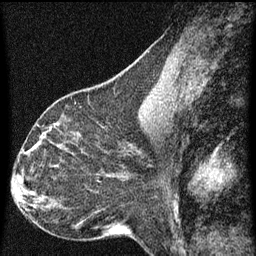
Breast MRI (dynamic contrast-enhanced), one sagittal slice. Slice 31 of 60 in the series (ordered by position). Dynamic contrast-enhanced series, image 2 of 3 at this slice position (ordered by acquisition). 1.5 T. TE 4.2 ms, TR 8 ms. 256 × 256 image matrix. Patient: female, 44 years.
Outlined on this slice (semi-automatically segmented with operator editing):
- analysis volume of interest (the breast-tissue region the enhancement analysis was run in; not a lesion): bounding box (x1, y1, x2, y2) in pixels: (49, 128, 95, 169)
- tumour enhancement mask (voxels above the 70 % enhancement threshold inside the analysis volume of interest): (49, 128, 56, 167)